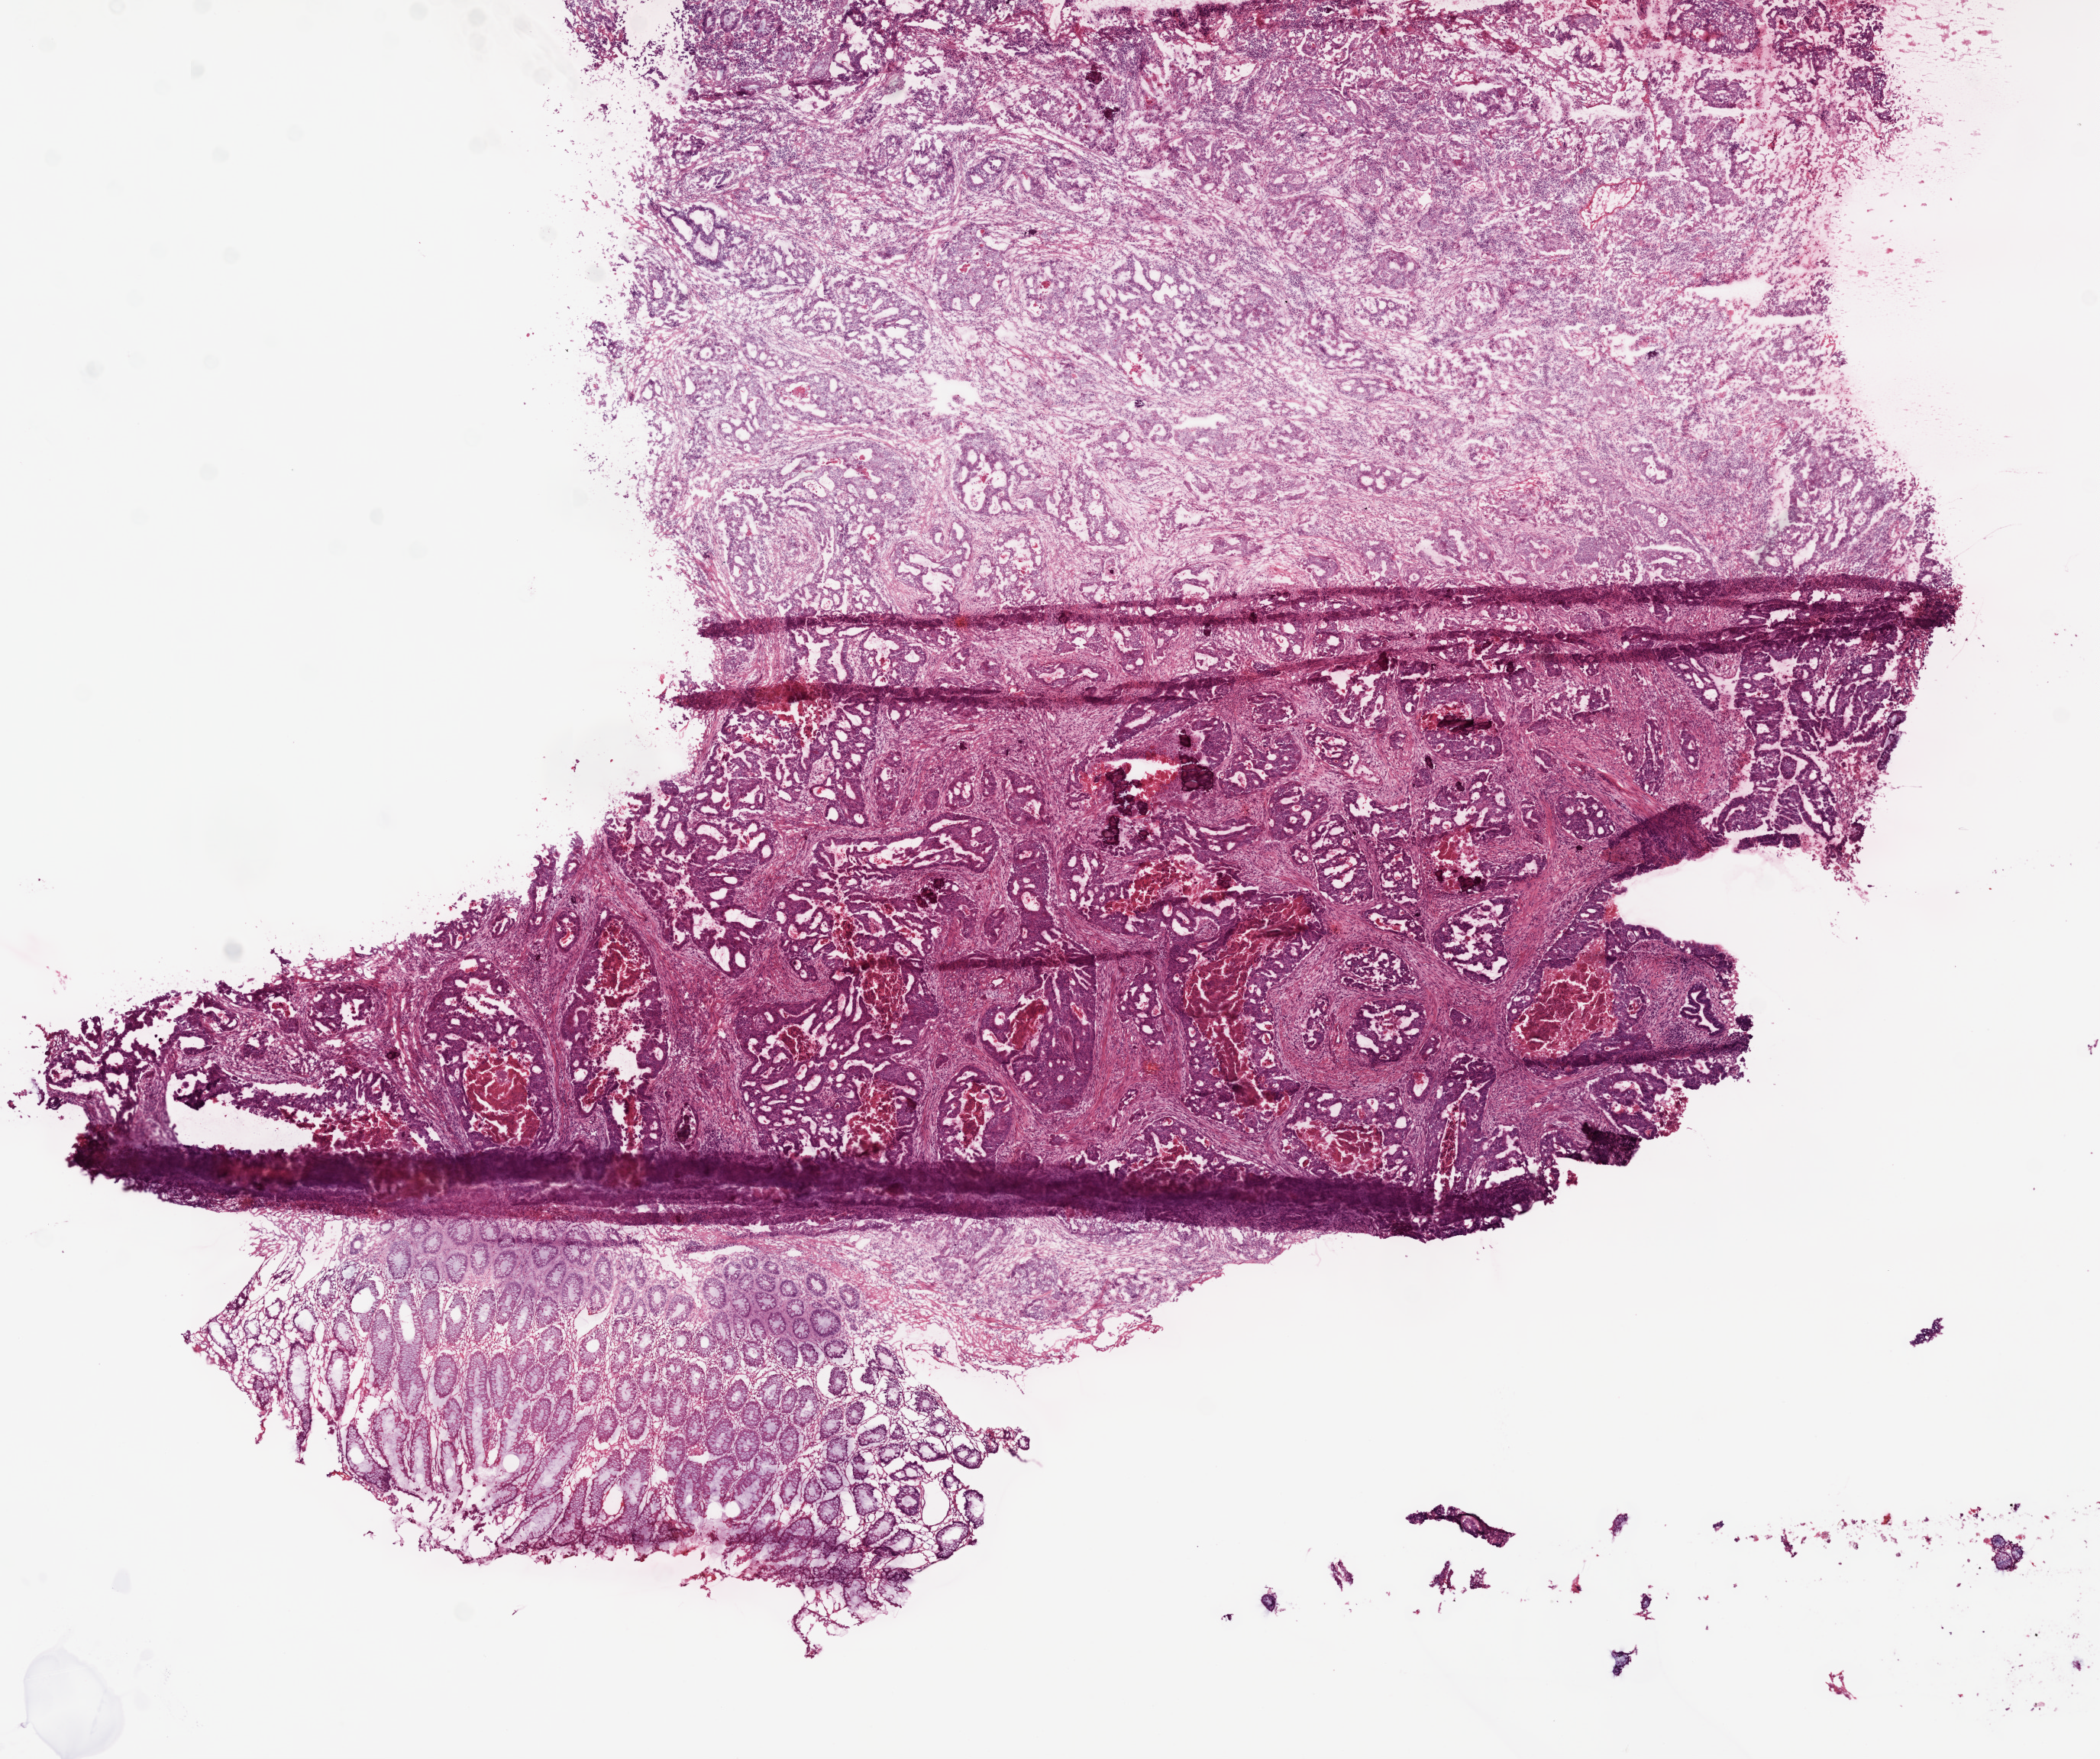
H&E whole-slide image, shown as a low-resolution overview of the whole scanned area (about 11.0 x 9.2 mm, from a 20x scan). Frozen section from the top of the tissue portion. Colon, primary tumour sample. Male, age 49 years at initial diagnosis. Pathologist review of this section (percent, as recorded): tumour cells 60%, tumour nuclei 75%, normal cells 10%, stromal cells 15%, necrosis 15%.
• lymph nodes positive (case pathology): 10 of 12 examined
• TNM: T3 N2 M1
• diagnosis: Adenocarcinoma, NOS (rectosigmoid junction)
• AJCC pathologic stage: IVA